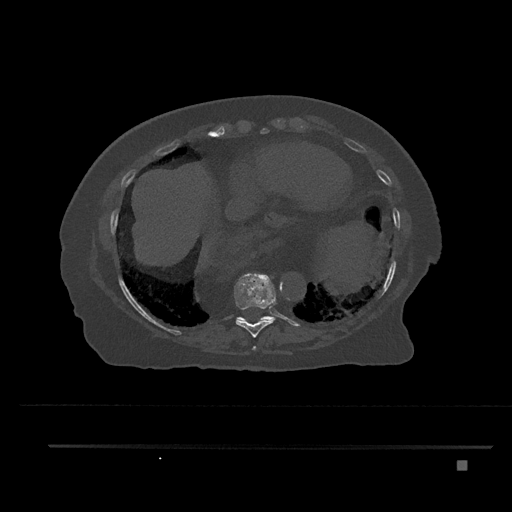
CT including the spine, one axial slice; position 389 of 797 along the scan axis; bone window (W 1800 / L 400 HU); 0.5 mm slice thickness; 512 × 512 image matrix, field of view 437 × 437 mm. Female patient, age 76 years. Case-level facts recorded for this patient, not image findings: primary cancer: lung; vertebrae with lytic lesions (as recorded): T11, L3.
Structures marked on this image (semi-automatically segmented with operator editing):
- T10 vertebra: box from (x=237, y=316) to (x=273, y=322) px
- T8 vertebra: (x=252, y=346)–(x=257, y=351)
- T9 vertebra: (x=234, y=274)–(x=276, y=337)